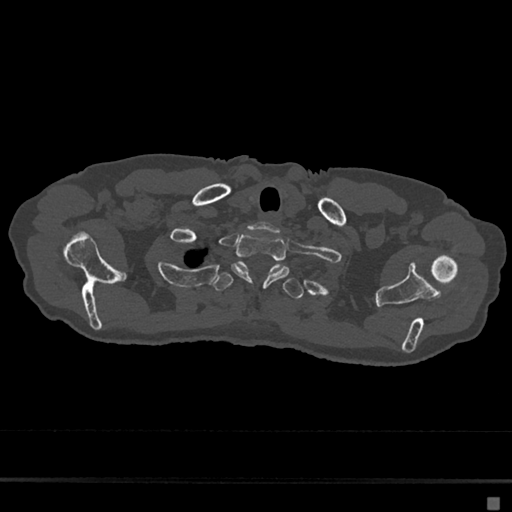
CT including the spine, one axial slice. Position 599 of 797 along the scan axis. Reconstruction kernel Br40s/3. 120 kVp. Bone window (W 1800 / L 400 HU). 0.5 mm slice thickness. 512 × 512 image matrix, field of view 360 × 360 mm. Female patient, age 68 years. From the clinical record (not read from this slice): primary cancer: renal.
Structures marked on this image (semi-automatically segmented with operator editing):
- T1 vertebra: bounding box <231,234,290,287> (left, top, right, bottom; pixels)
- T2 vertebra: <212,263,304,299>